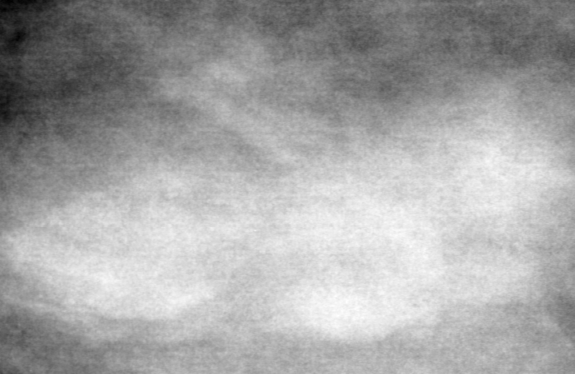
Region of interest cut from a scanned film mammogram (one marked finding), right breast, MLO view, BI-RADS breast density category 4 (scale 1–4).
- Marked abnormality: mass, shape lobulated, margins obscured; BI-RADS assessment category 4; pathology result (as recorded, not read from the image): benign.